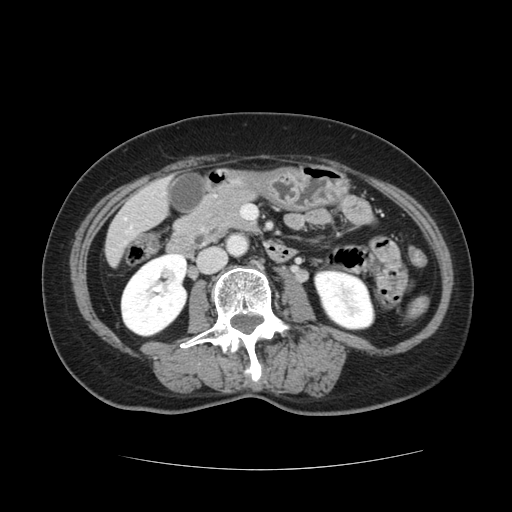
Contrast-enhanced abdominal CT, one axial slice. 120 kVp. Intravenous contrast given. Soft-tissue window (W 400 / L 40 HU). 512 × 512 image matrix, field of view 366 × 366 mm. Female patient, age 67 years. From the clinical record (not read from this slice): diagnosis: colorectal cancer liver metastases, imaged before liver resection; multiple liver metastases: yes; largest metastasis: 3 cm.
Structures marked on this image (outlined manually by an expert reader):
- liver: box from (x=106, y=181) to (x=168, y=262) px
- planned liver remnant (the part of the liver to remain after resection): (x=106, y=211)–(x=138, y=262)